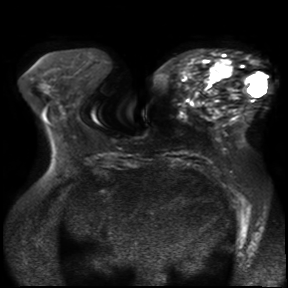
Breast MRI, one axial slice. Position 13 of 30 along the scan axis. Diffusion-weighted series; image 2 of 4 stored at this slice position (different b-values; order by instance number). 3 T. 288 × 288 image matrix, field of view 360 × 360 mm. Female patient.
Structures marked on this image (manually delineated by an expert):
- tumour on diffusion-weighted imaging: box from (x=207, y=58) to (x=233, y=80) px